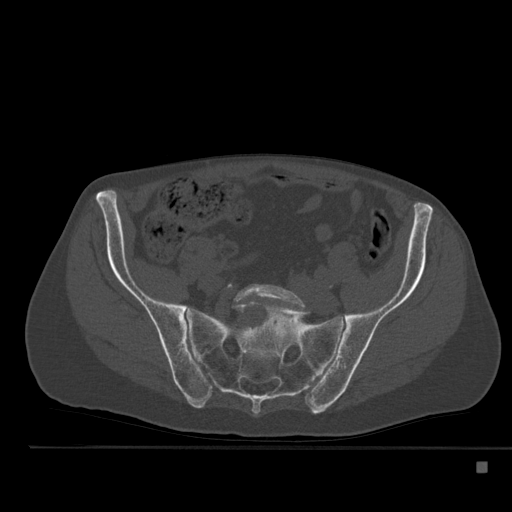
CT including the spine, one axial slice. Position 99 of 517 along the scan axis. Reconstruction kernel Br40s. 120 kVp. Bone window (W 1800 / L 400 HU). 512 × 512 image matrix, field of view 408 × 408 mm. Patient: male, 70 years. Case-level facts recorded for this patient, not image findings: primary cancer: renal; vertebrae with lytic lesions (as recorded): T4, T6, T10, T12, L3, L4, L5.
Outlined on this slice (semi-automatically segmented with operator editing):
- L5 vertebra: bounding box <233,284,307,309> (left, top, right, bottom; pixels)